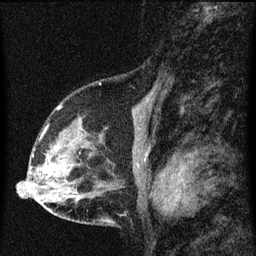
Breast MRI (dynamic contrast-enhanced), one sagittal slice; slice 39 of 60 in the series (ordered by position); dynamic contrast-enhanced series, image 2 of 3 at this slice position (ordered by acquisition); 1.5 T; TE 4.2 ms, TR 8 ms; 2 mm slice thickness; 256 × 256 image matrix, field of view 180 × 180 mm. Female patient, age 56 years.
Structures marked on this image (semi-automatic segmentation, software-assisted and operator-edited):
- analysis volume of interest (the breast-tissue region the enhancement analysis was run in; not a lesion): box from (x=34, y=114) to (x=102, y=181) px
- tumour enhancement mask (voxels above the 70 % enhancement threshold inside the analysis volume of interest): (x=49, y=167)–(x=53, y=170)